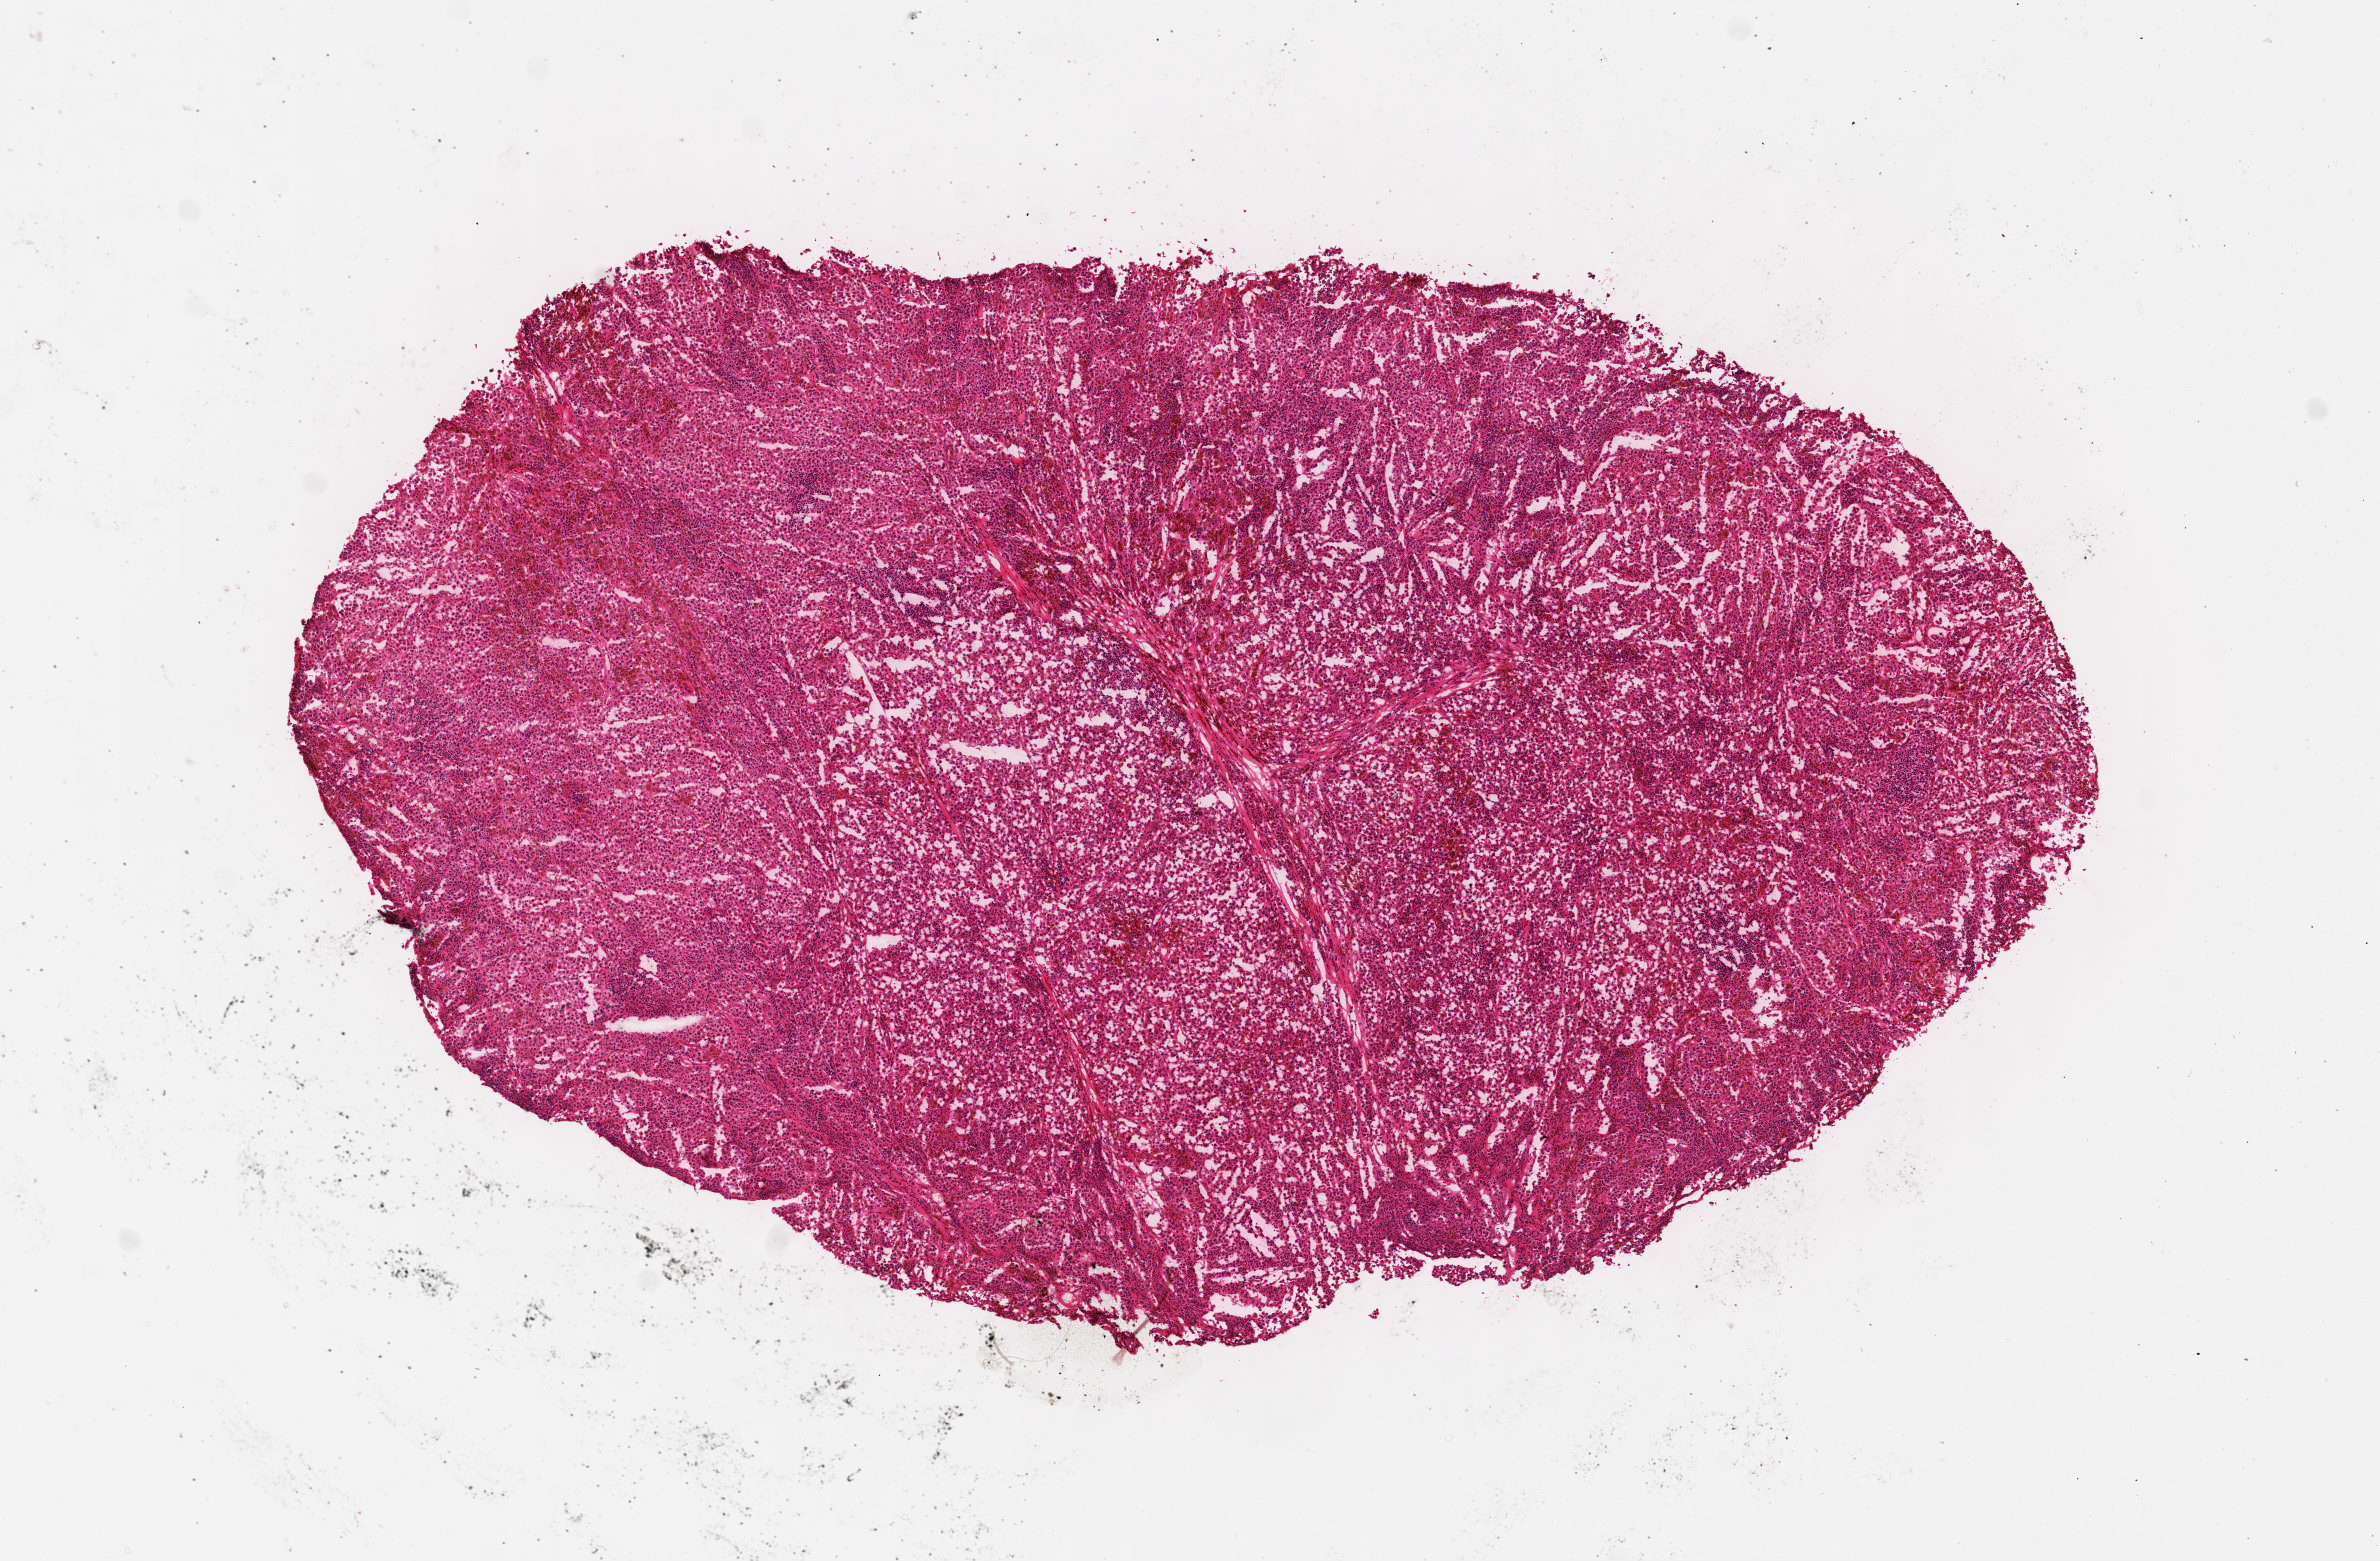
Whole-slide histology image, Hematoxylin and eosin (H&E) stained, shown as a low-resolution overview of the whole scanned area (about 9.4 x 6.1 mm, slide scanned at 40x), FFPE section, primary tumour sample from the skin. Male, age 54 years at initial diagnosis.
Diagnosis: Malignant melanoma, NOS.